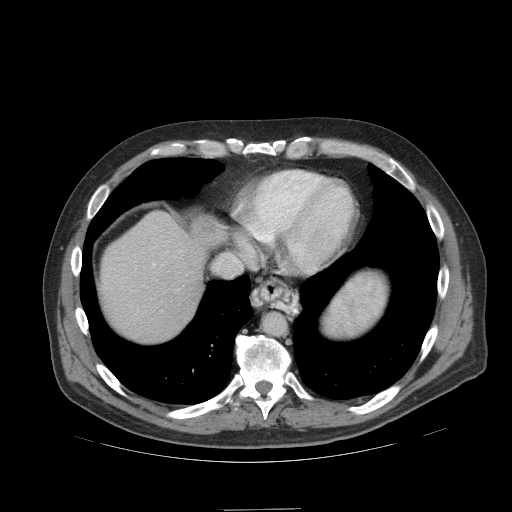
Contrast-enhanced abdominal CT (liver protocol), one axial slice; position 90 of 99 along the scan axis; reconstruction kernel STANDARD; 140 kVp; soft-tissue window (W 400 / L 40 HU); 2.5 mm slice thickness; 512 × 512 image matrix, field of view 440 × 440 mm. Case-level facts recorded for this patient, not image findings: diagnosis: hepatocellular carcinoma (patient treated with transarterial chemoembolisation; whether this scan precedes or follows treatment is not stated here); TNM stage (as recorded): Stage-I; Child-Pugh class: A; tumour differentiation: no biopsy; tumour nodularity: uninodular.
Outlined on this slice (semi-automatically segmented with operator editing):
- abdominal aorta: bounding box <263,313,286,335> (left, top, right, bottom; pixels)
- liver parenchyma outside the tumour (the mass and vessels are separate outlines, so this box may not span the whole liver): <100,212,224,342>
- mass: <195,220,215,238>
- liver vessels: <153,264,155,266>